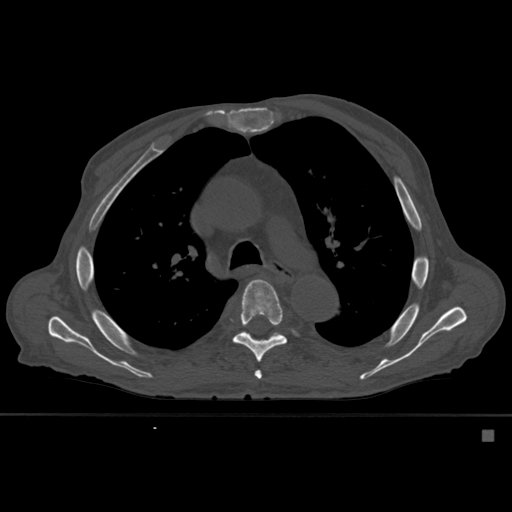
CT including the spine, one axial slice. Bone window (W 1800 / L 400 HU). 512 × 512 image matrix. Patient: male, 78 years. From the clinical record (not read from this slice): primary cancer: prostate.
Structures marked on this image (semi-automatically segmented with operator editing):
- T5 vertebra: bounding box <255,370,262,380> (left, top, right, bottom; pixels)
- T6 vertebra: <233,279,287,363>
- T7 vertebra: <244,331,279,336>